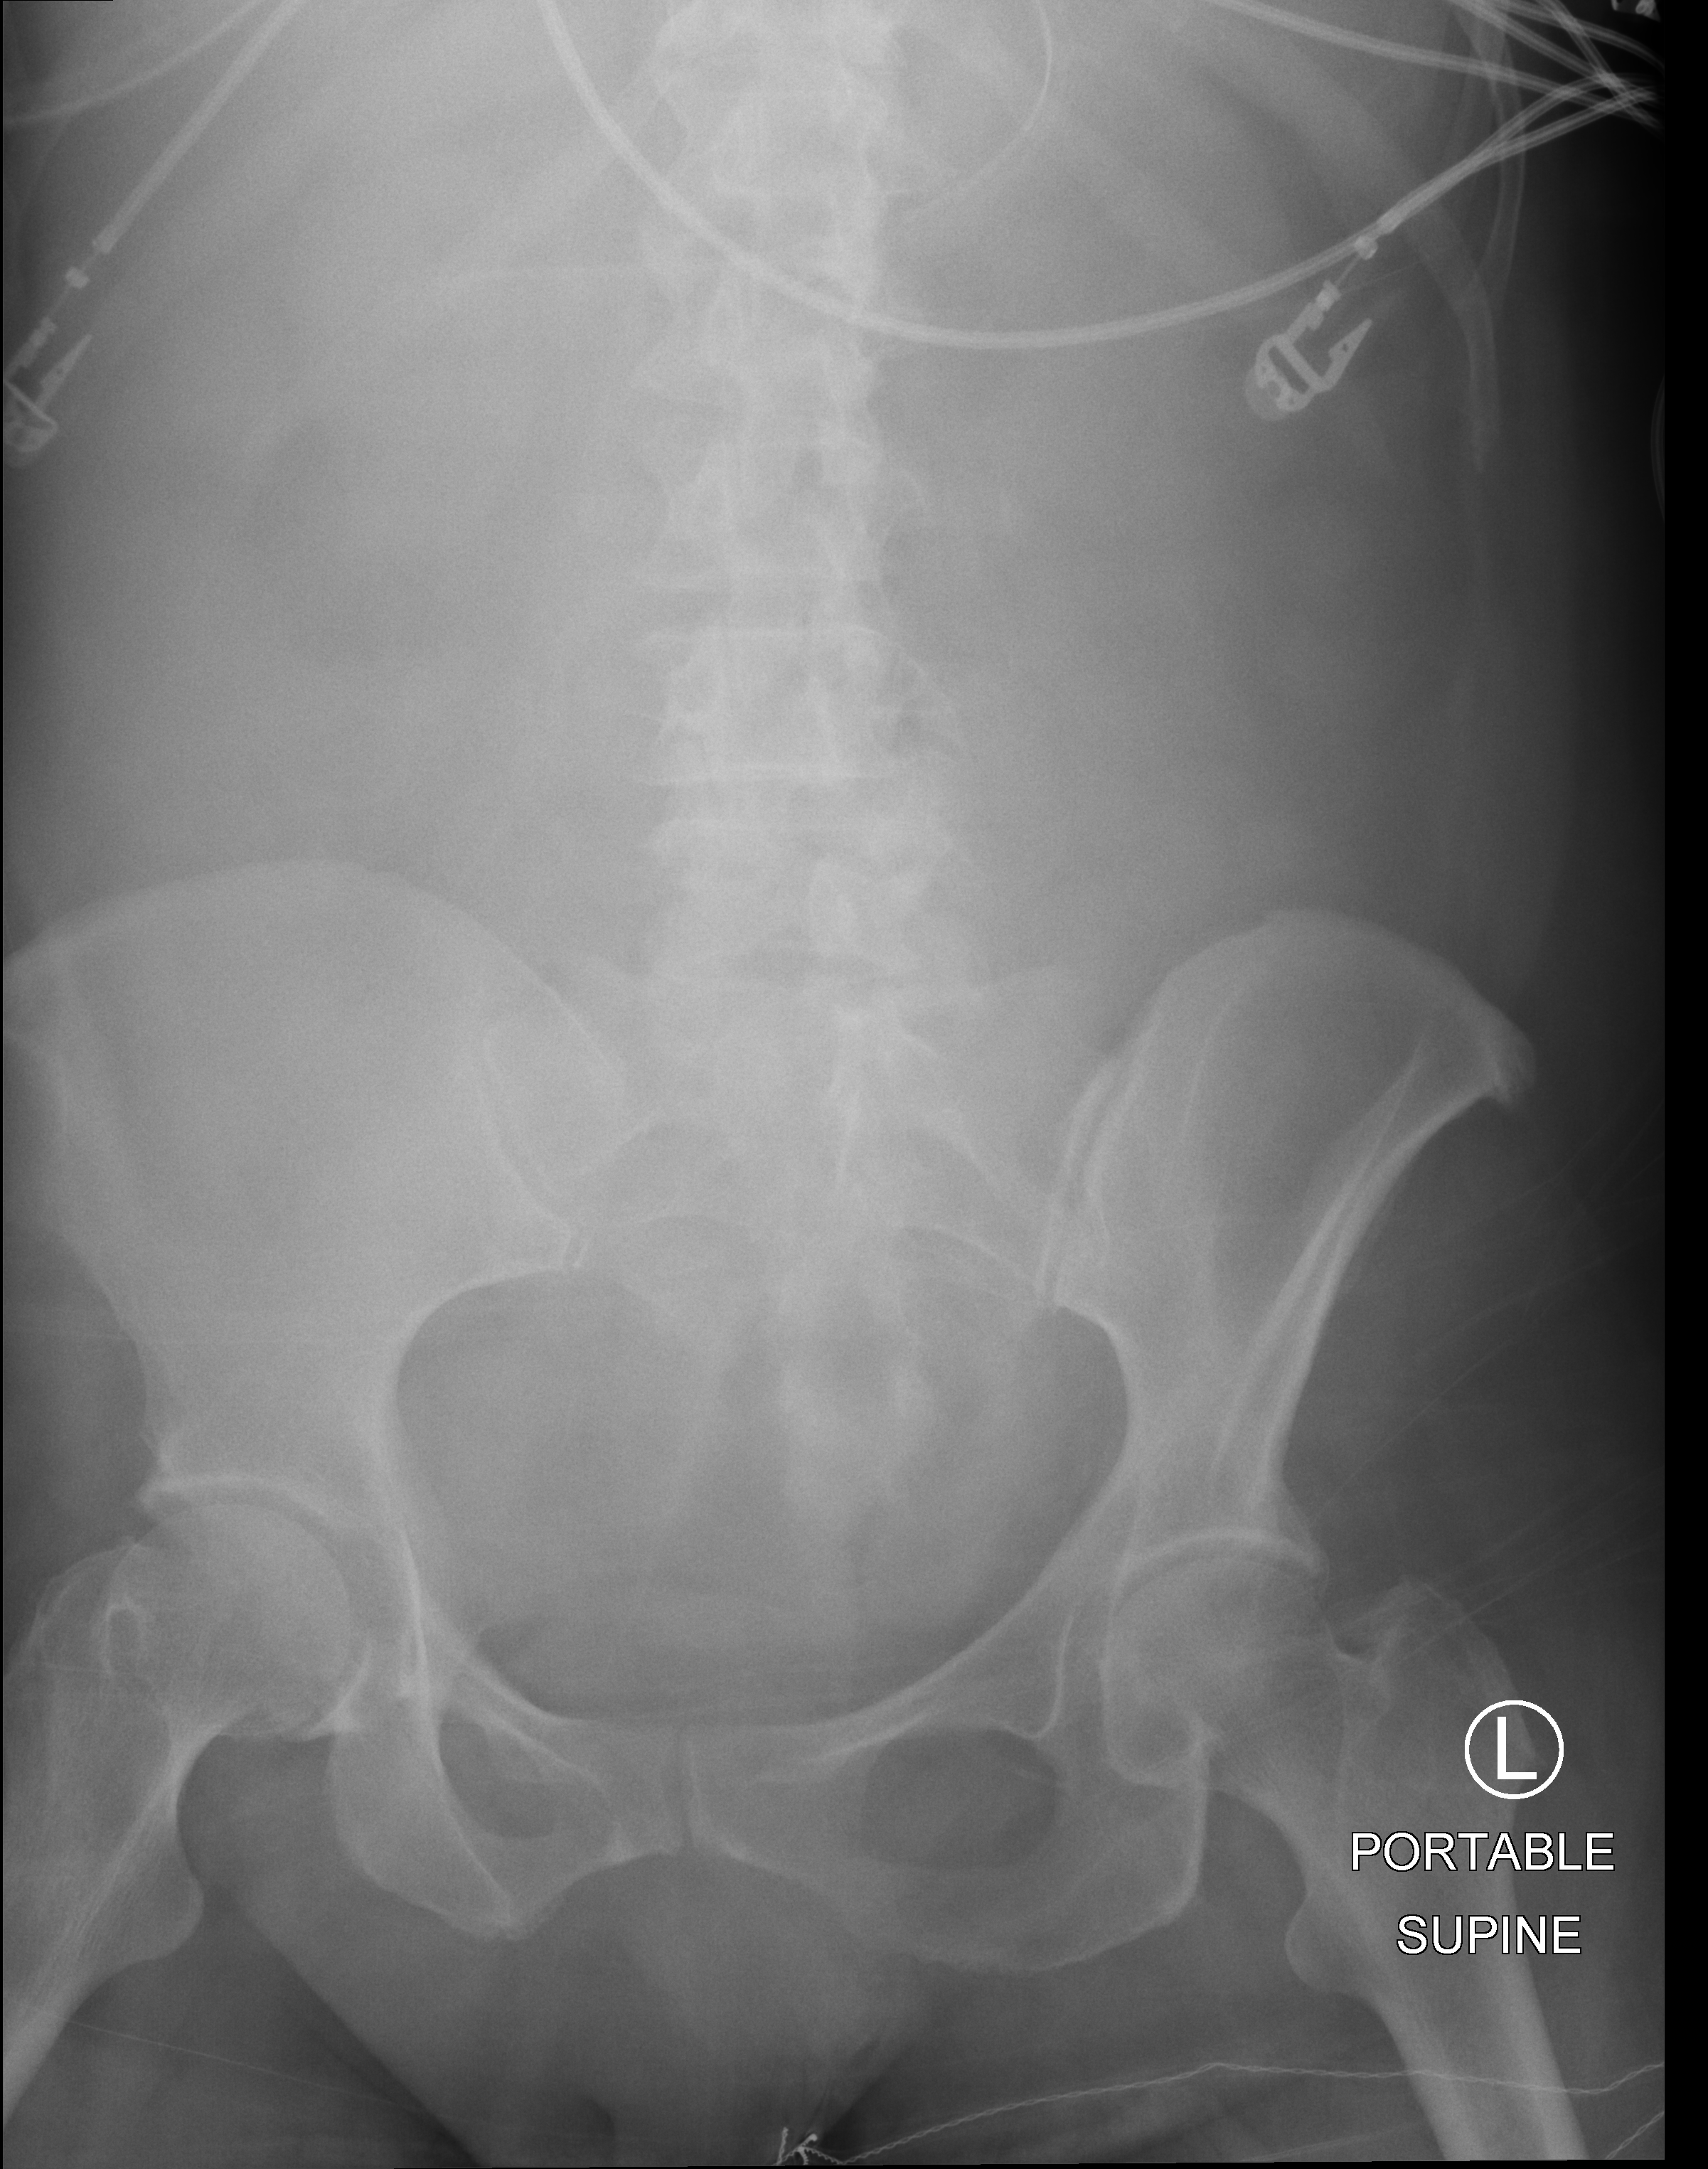
Abdomen X-ray (portable). Female patient hospitalised with COVID-19, age 60–74 years.
From the hospital-stay record, not from the radiograph (when in the stay this image was taken is not recorded): mechanically ventilated during this hospital stay: yes; admitted to intensive care during this hospital stay: yes; hypertension (admission record): yes.